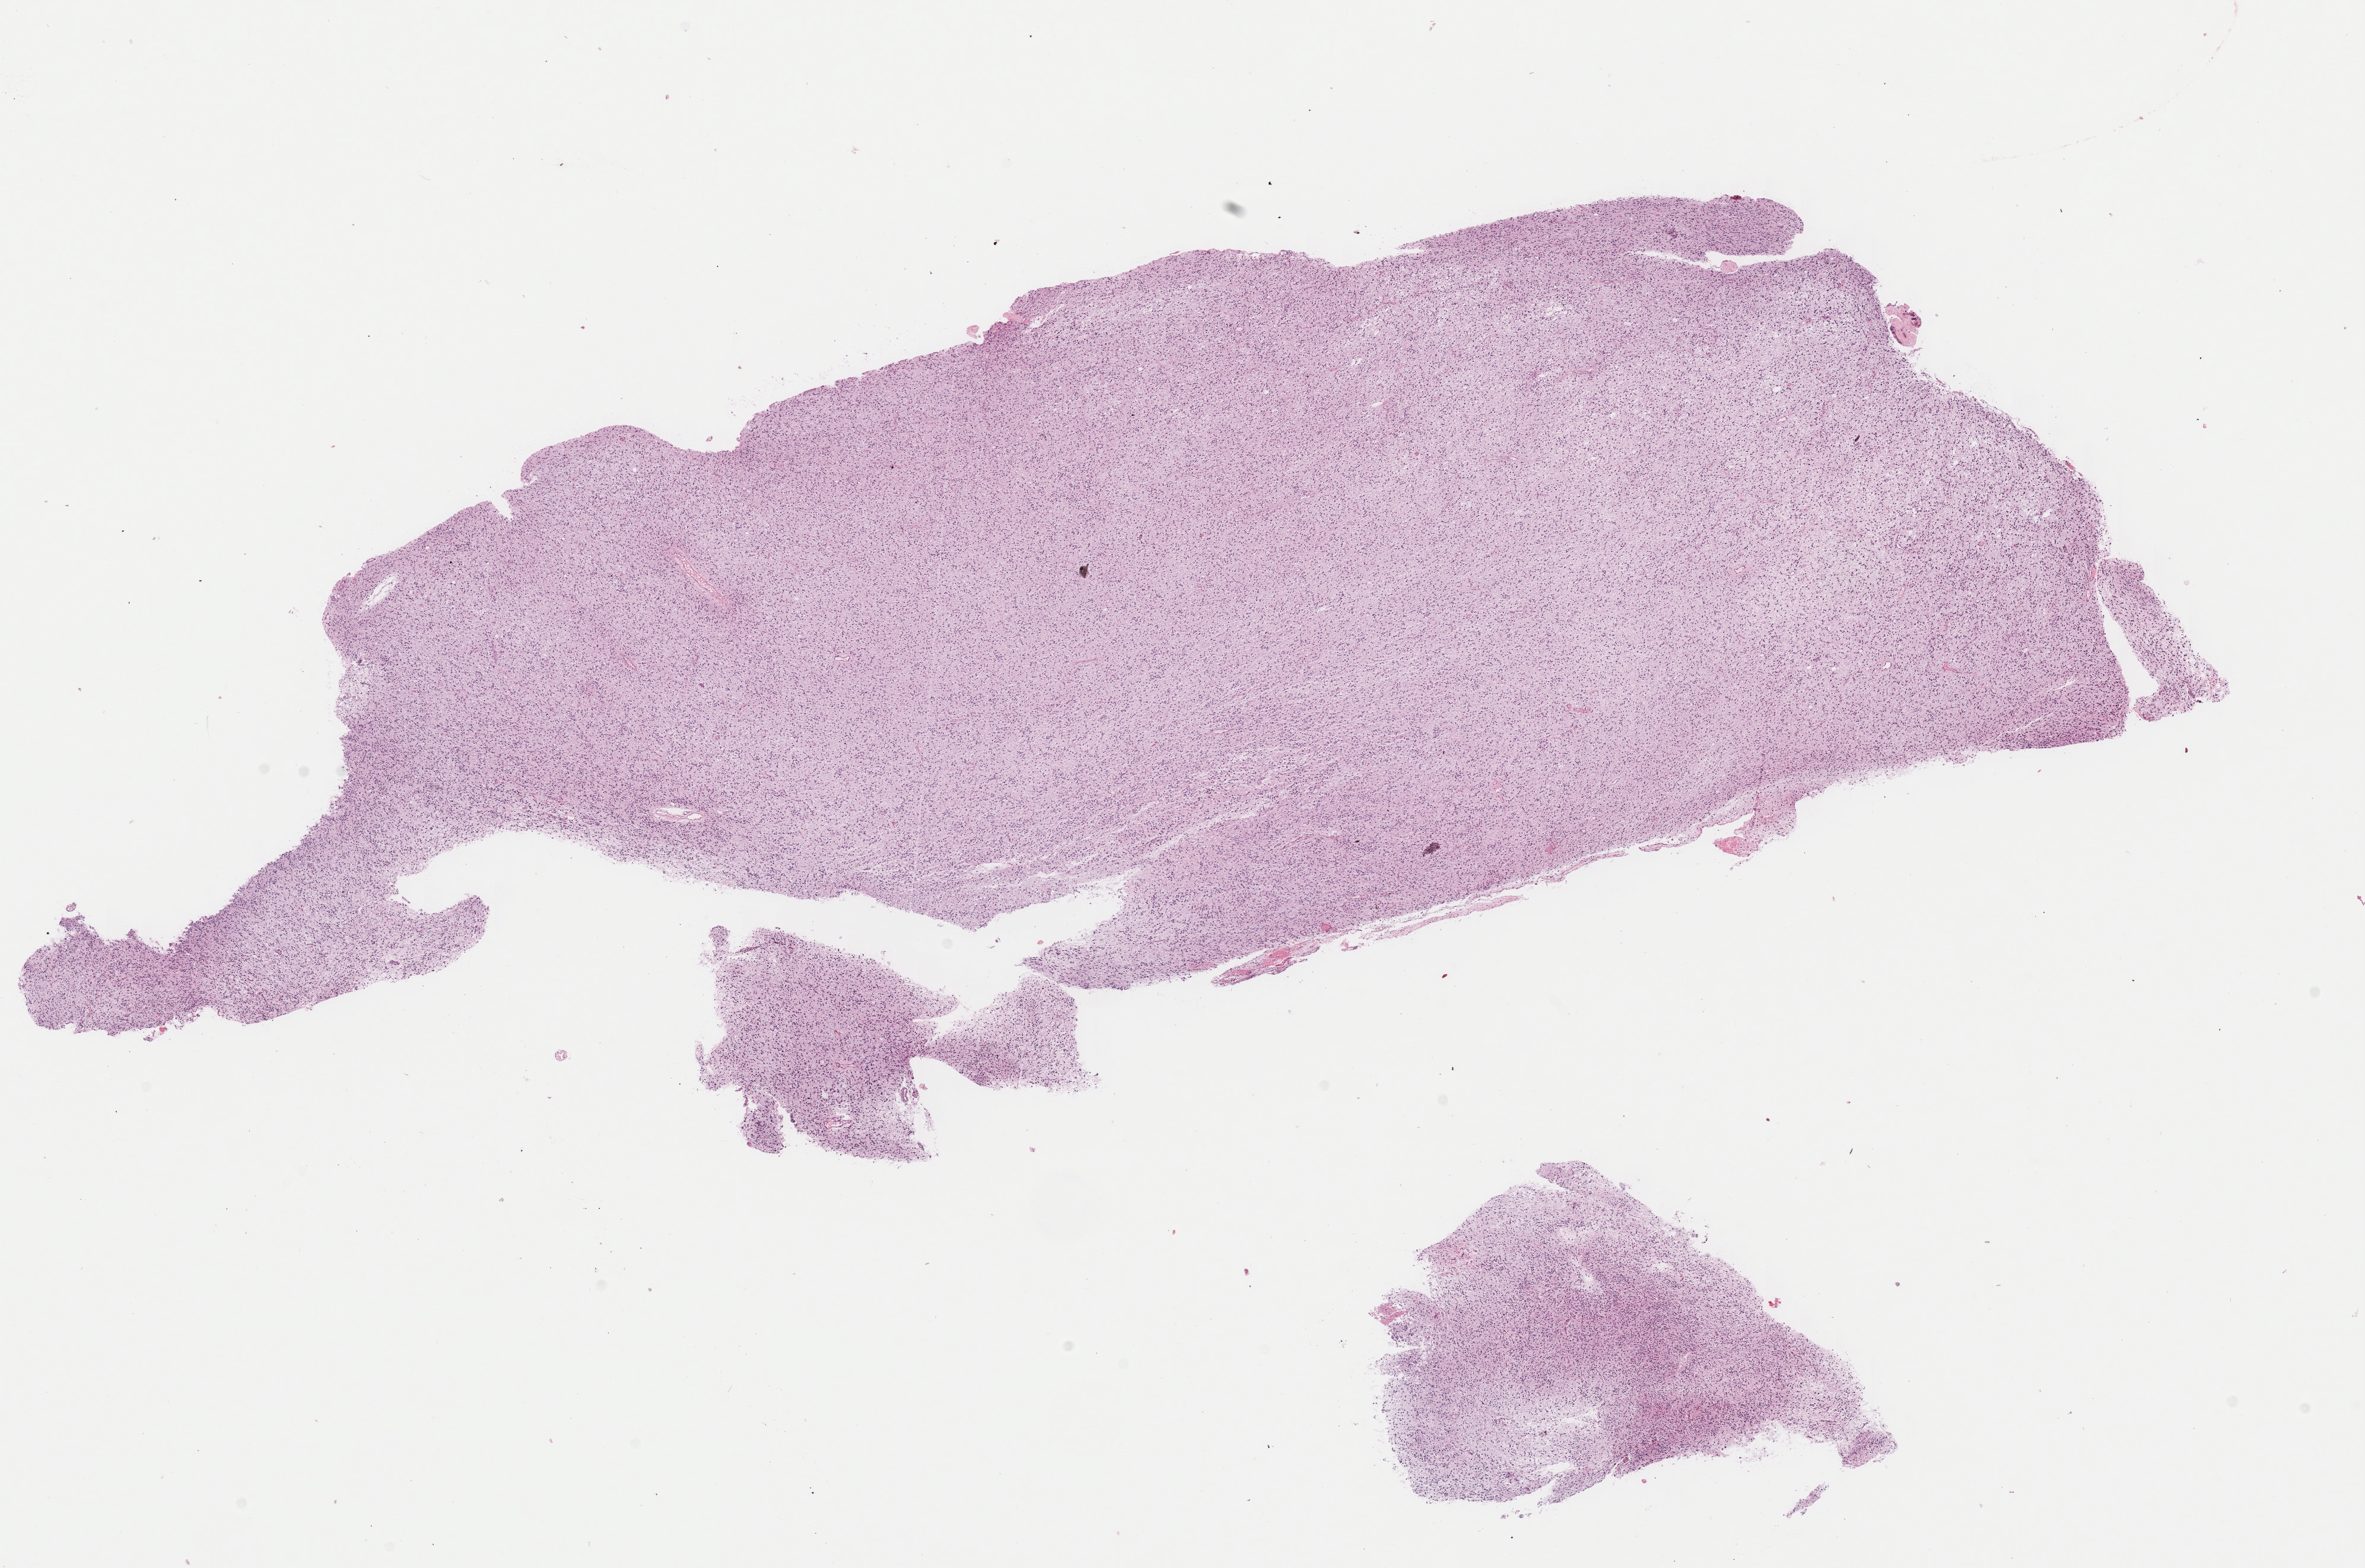
Digitized H&E-stained tissue section (whole slide) — whole scanned area (about 15.7 x 10.4 mm) shown as a low-resolution overview, formalin-fixed paraffin-embedded (FFPE) diagnostic section, sample: primary tumour, brain. Male patient; age at initial diagnosis 32 years. Histologic grade: G3 (poorly differentiated).
• histologic diagnosis: Astrocytoma, anaplastic (temporal lobe)
• laterality: right